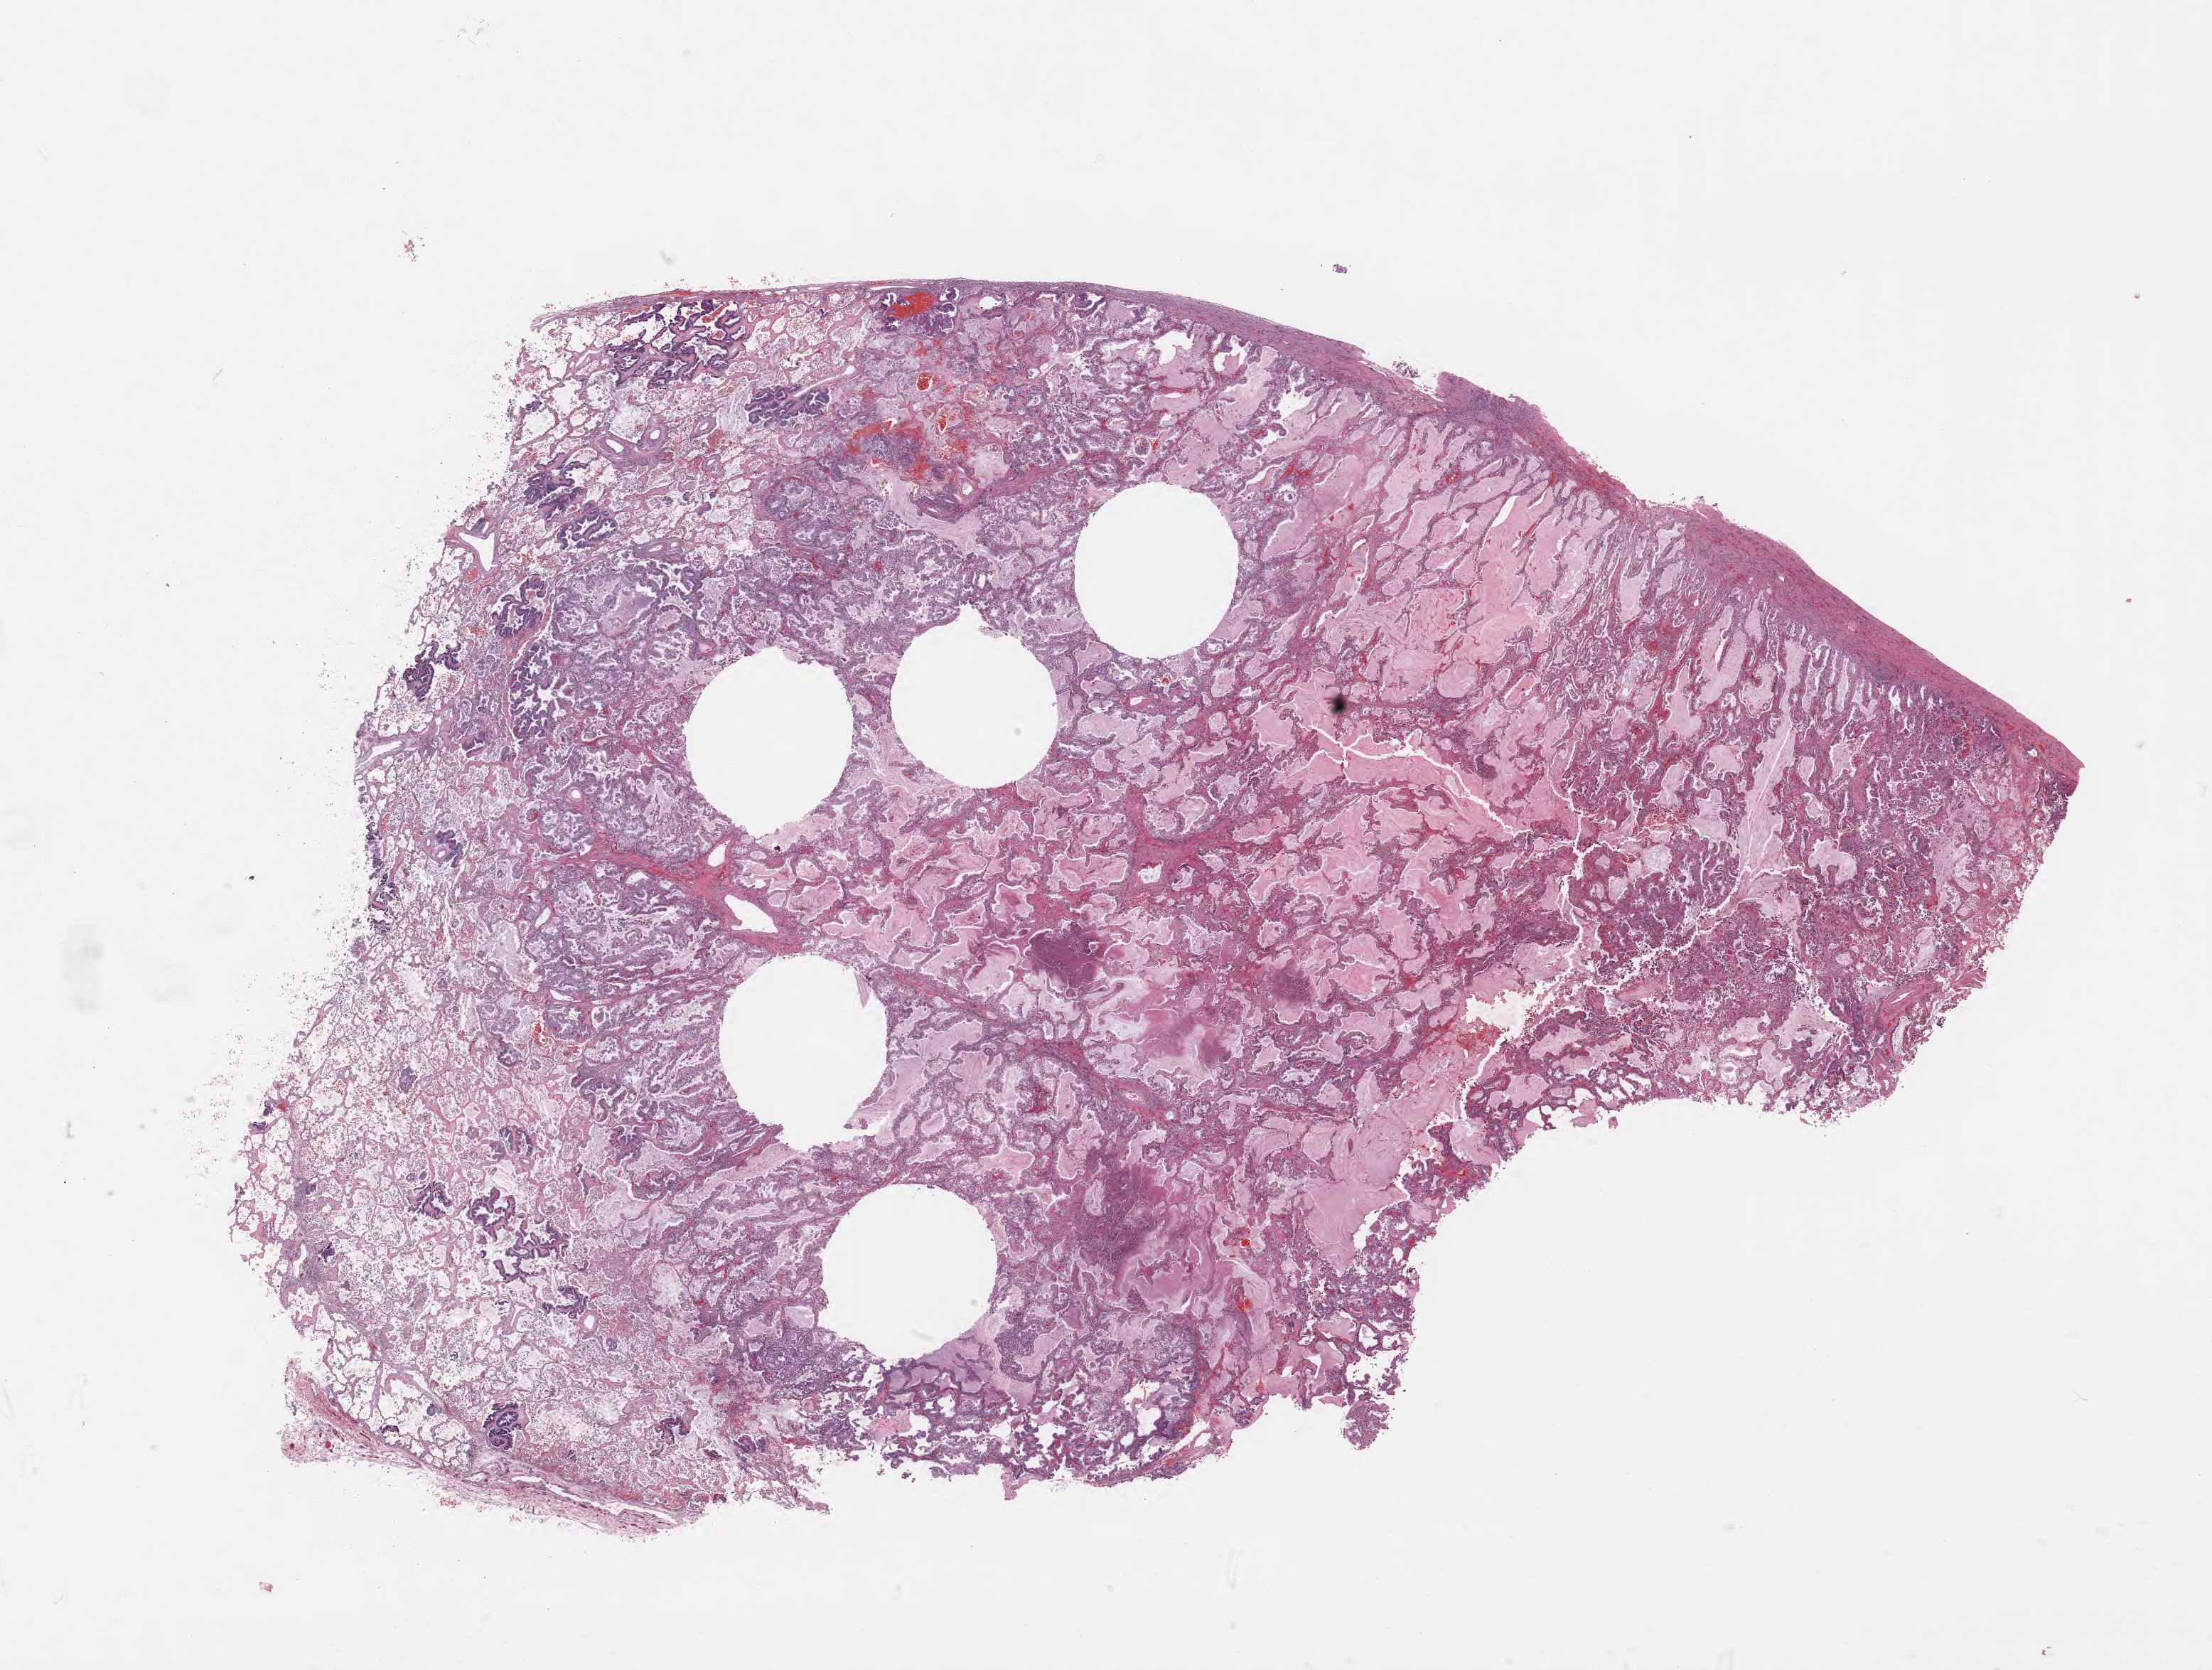
Whole-slide image, haematoxylin and eosin stain — a low-resolution overview of the entire scanned area, about 25.1 x 19.0 mm, specimen: tumor tissue, anatomic site: lung. Patient sex: male.
Histologic diagnosis: Adenocarcinoma, NOS.